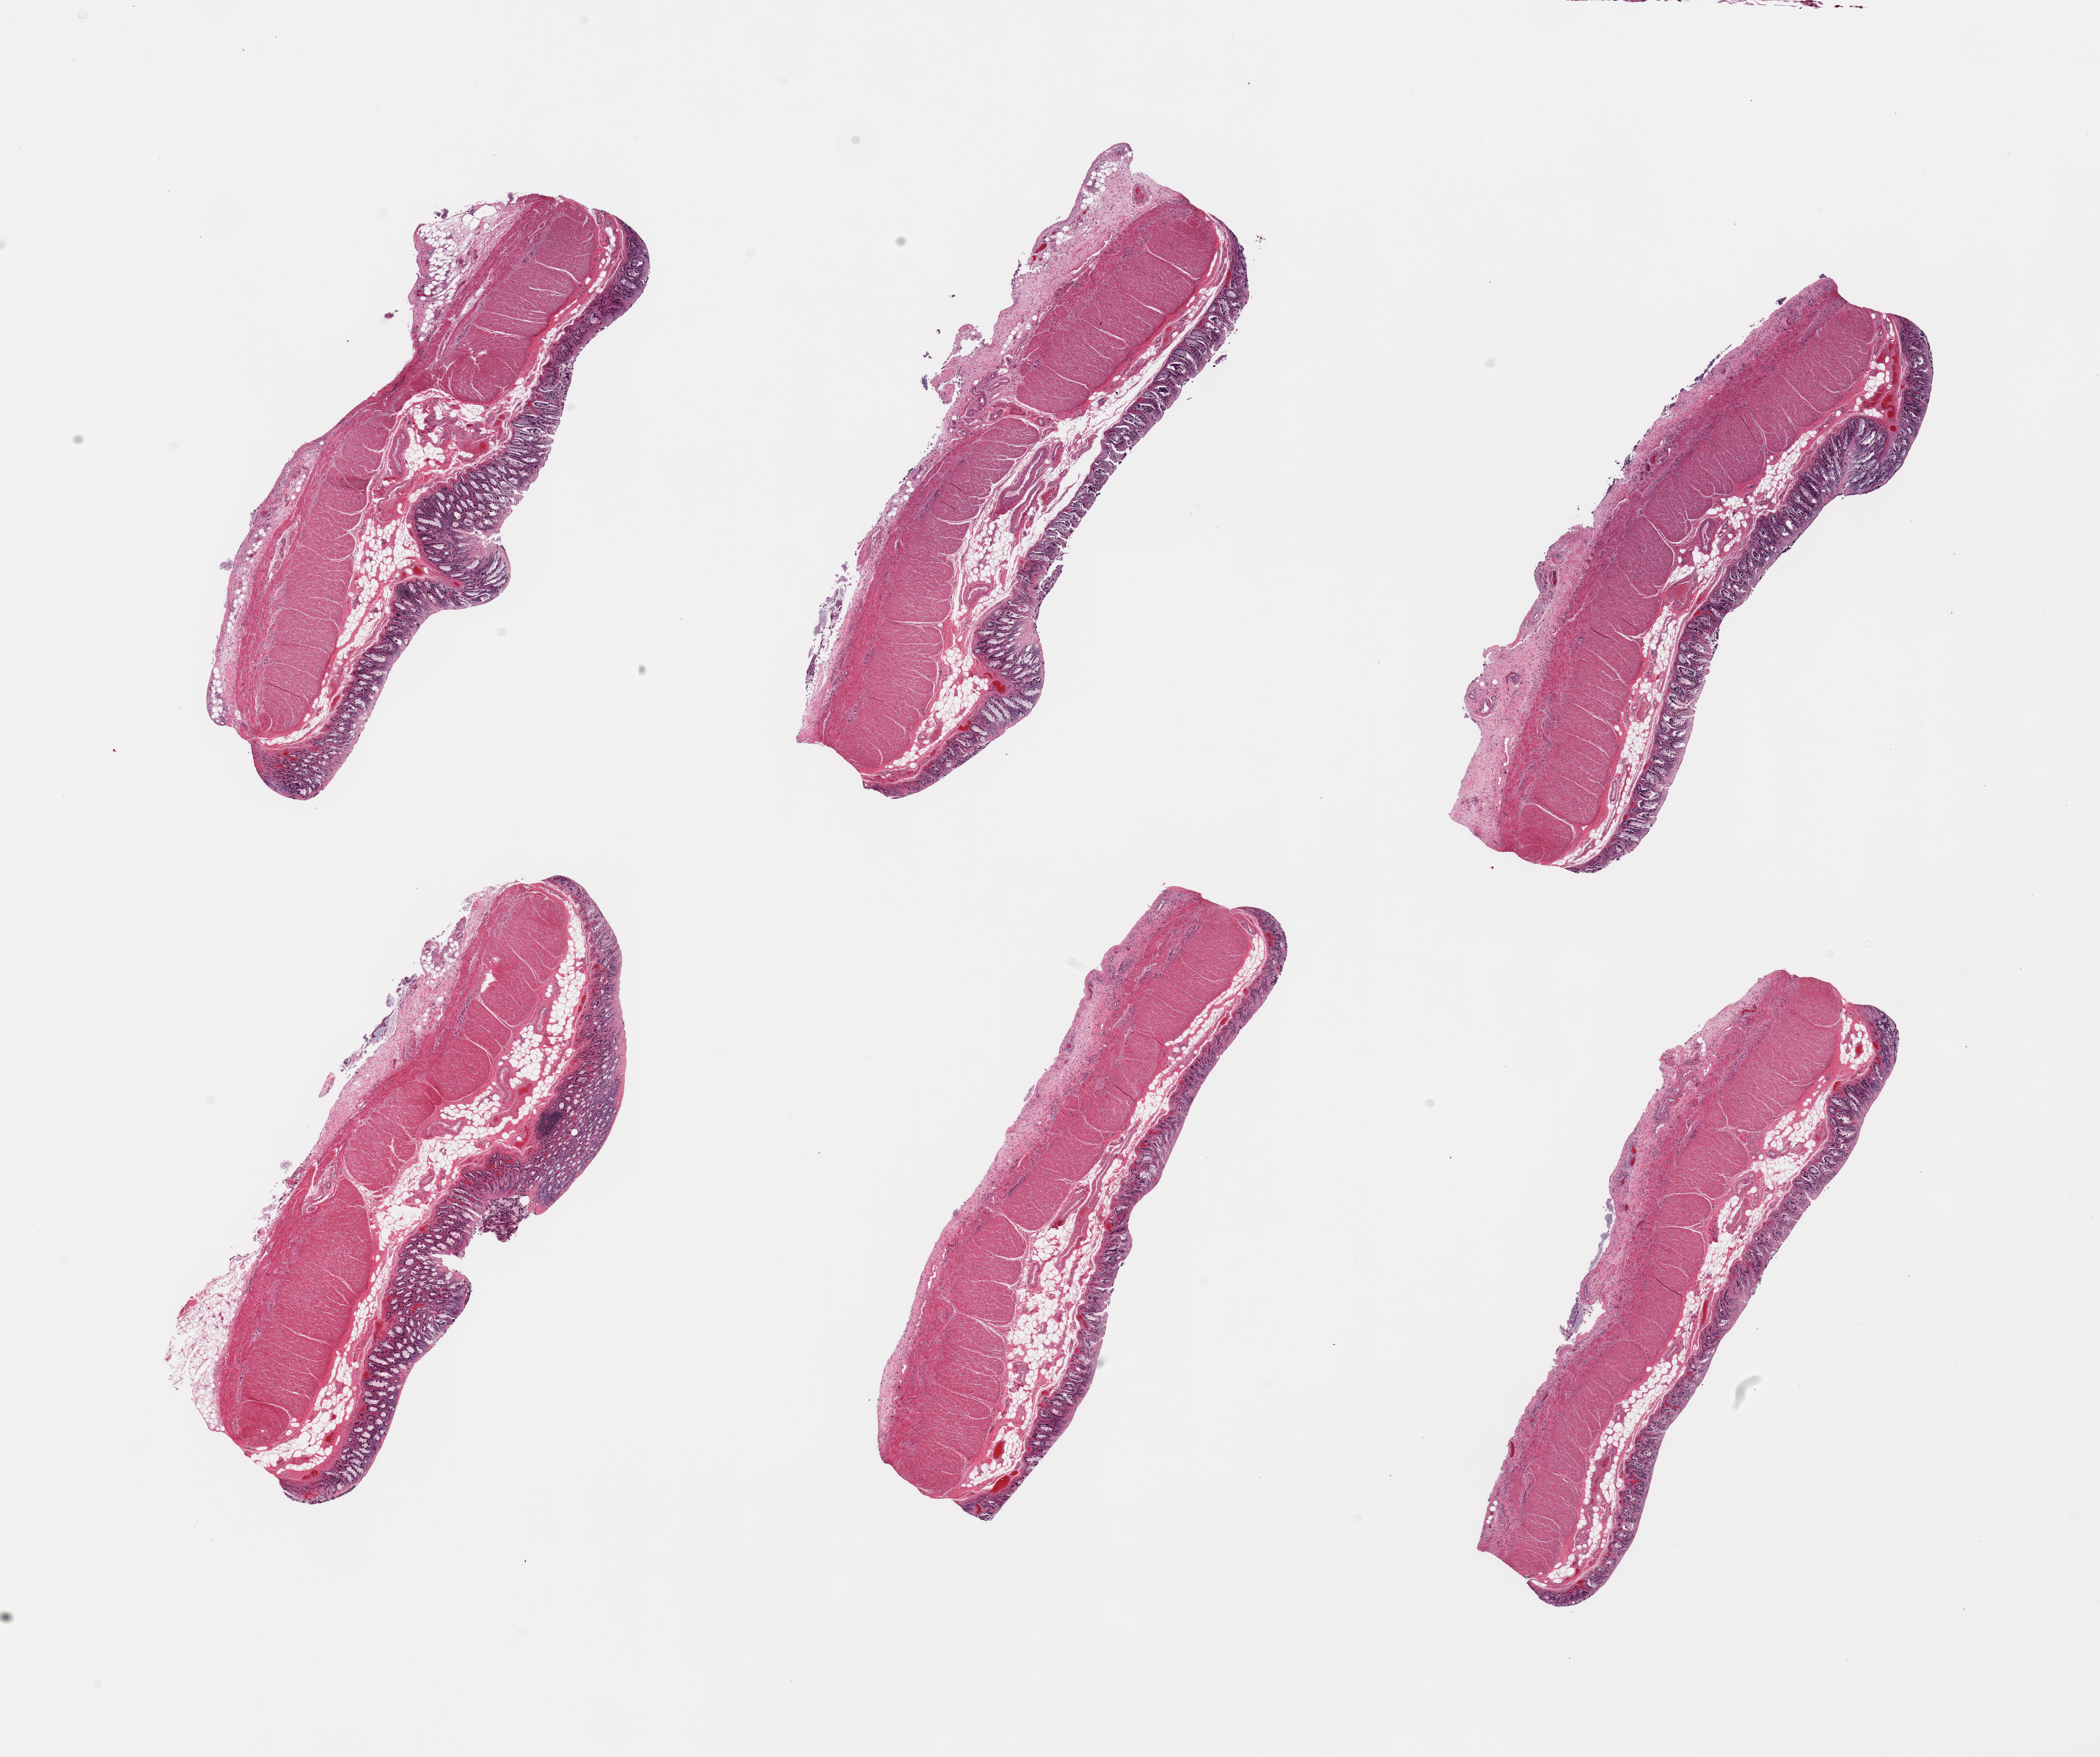
Haematoxylin and eosin whole-slide image, a low-resolution overview of the entire scanned area, about 22.6 x 18.9 mm (acquisition: 20x scan). PAXgene-fixed paraffin-embedded (PFPE) section. Target tissue: transverse colon. Tissue donor sample.
Review note (as recorded): 6 pieces; full thickness sections, moderate to severe autolysis, serositis.